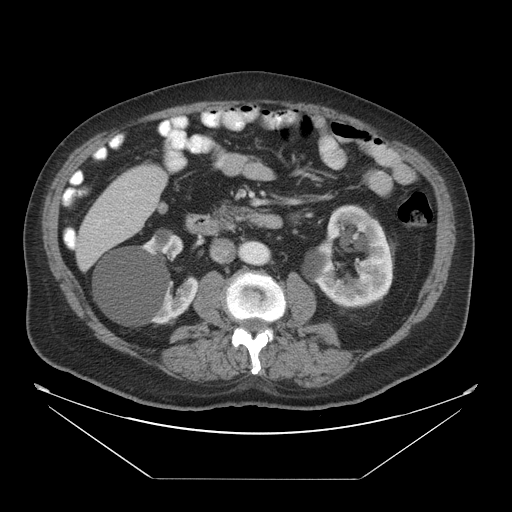
Contrast-enhanced abdominal CT, one axial slice. Reconstruction kernel STANDARD. 120 kVp. Intravenous contrast given. Soft-tissue window (W 400 / L 40 HU). 512 × 512 image matrix, field of view 463 × 463 mm. Male patient, age 87 years. Case-level facts recorded for this patient, not image findings: diagnosis: colorectal cancer liver metastases, imaged before liver resection; multiple liver metastases: no; largest metastasis: 4.5 cm; disease in both lobes: yes.
Outlined on this slice (outlined manually by an expert reader):
- liver: bounding box <76,165,168,272> (left, top, right, bottom; pixels)